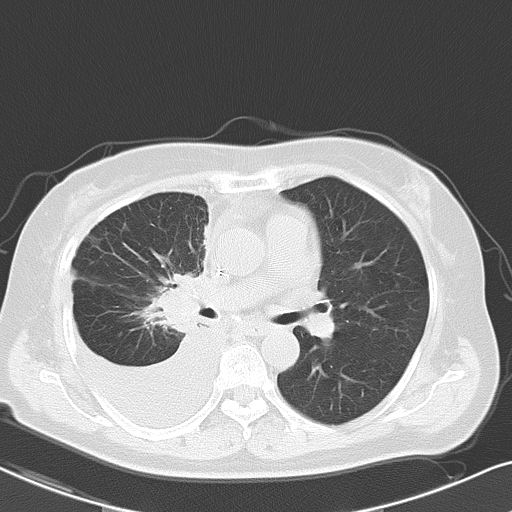
Chest CT, one axial slice; slice 29 of 48 in the series (ordered by position); reconstruction kernel B70f; lung window (W 1500 / L -600 HU); 512 × 512 image matrix. Patient: female, 69 years. From the clinical record (not read from this slice): clinical TNM (as recorded): T2a N0 M1c.
Outlined on this slice (bounding box drawn by a radiologist):
- lung tumour (recorded histology: adenocarcinoma): bounding box <145,262,206,334> (left, top, right, bottom; pixels)